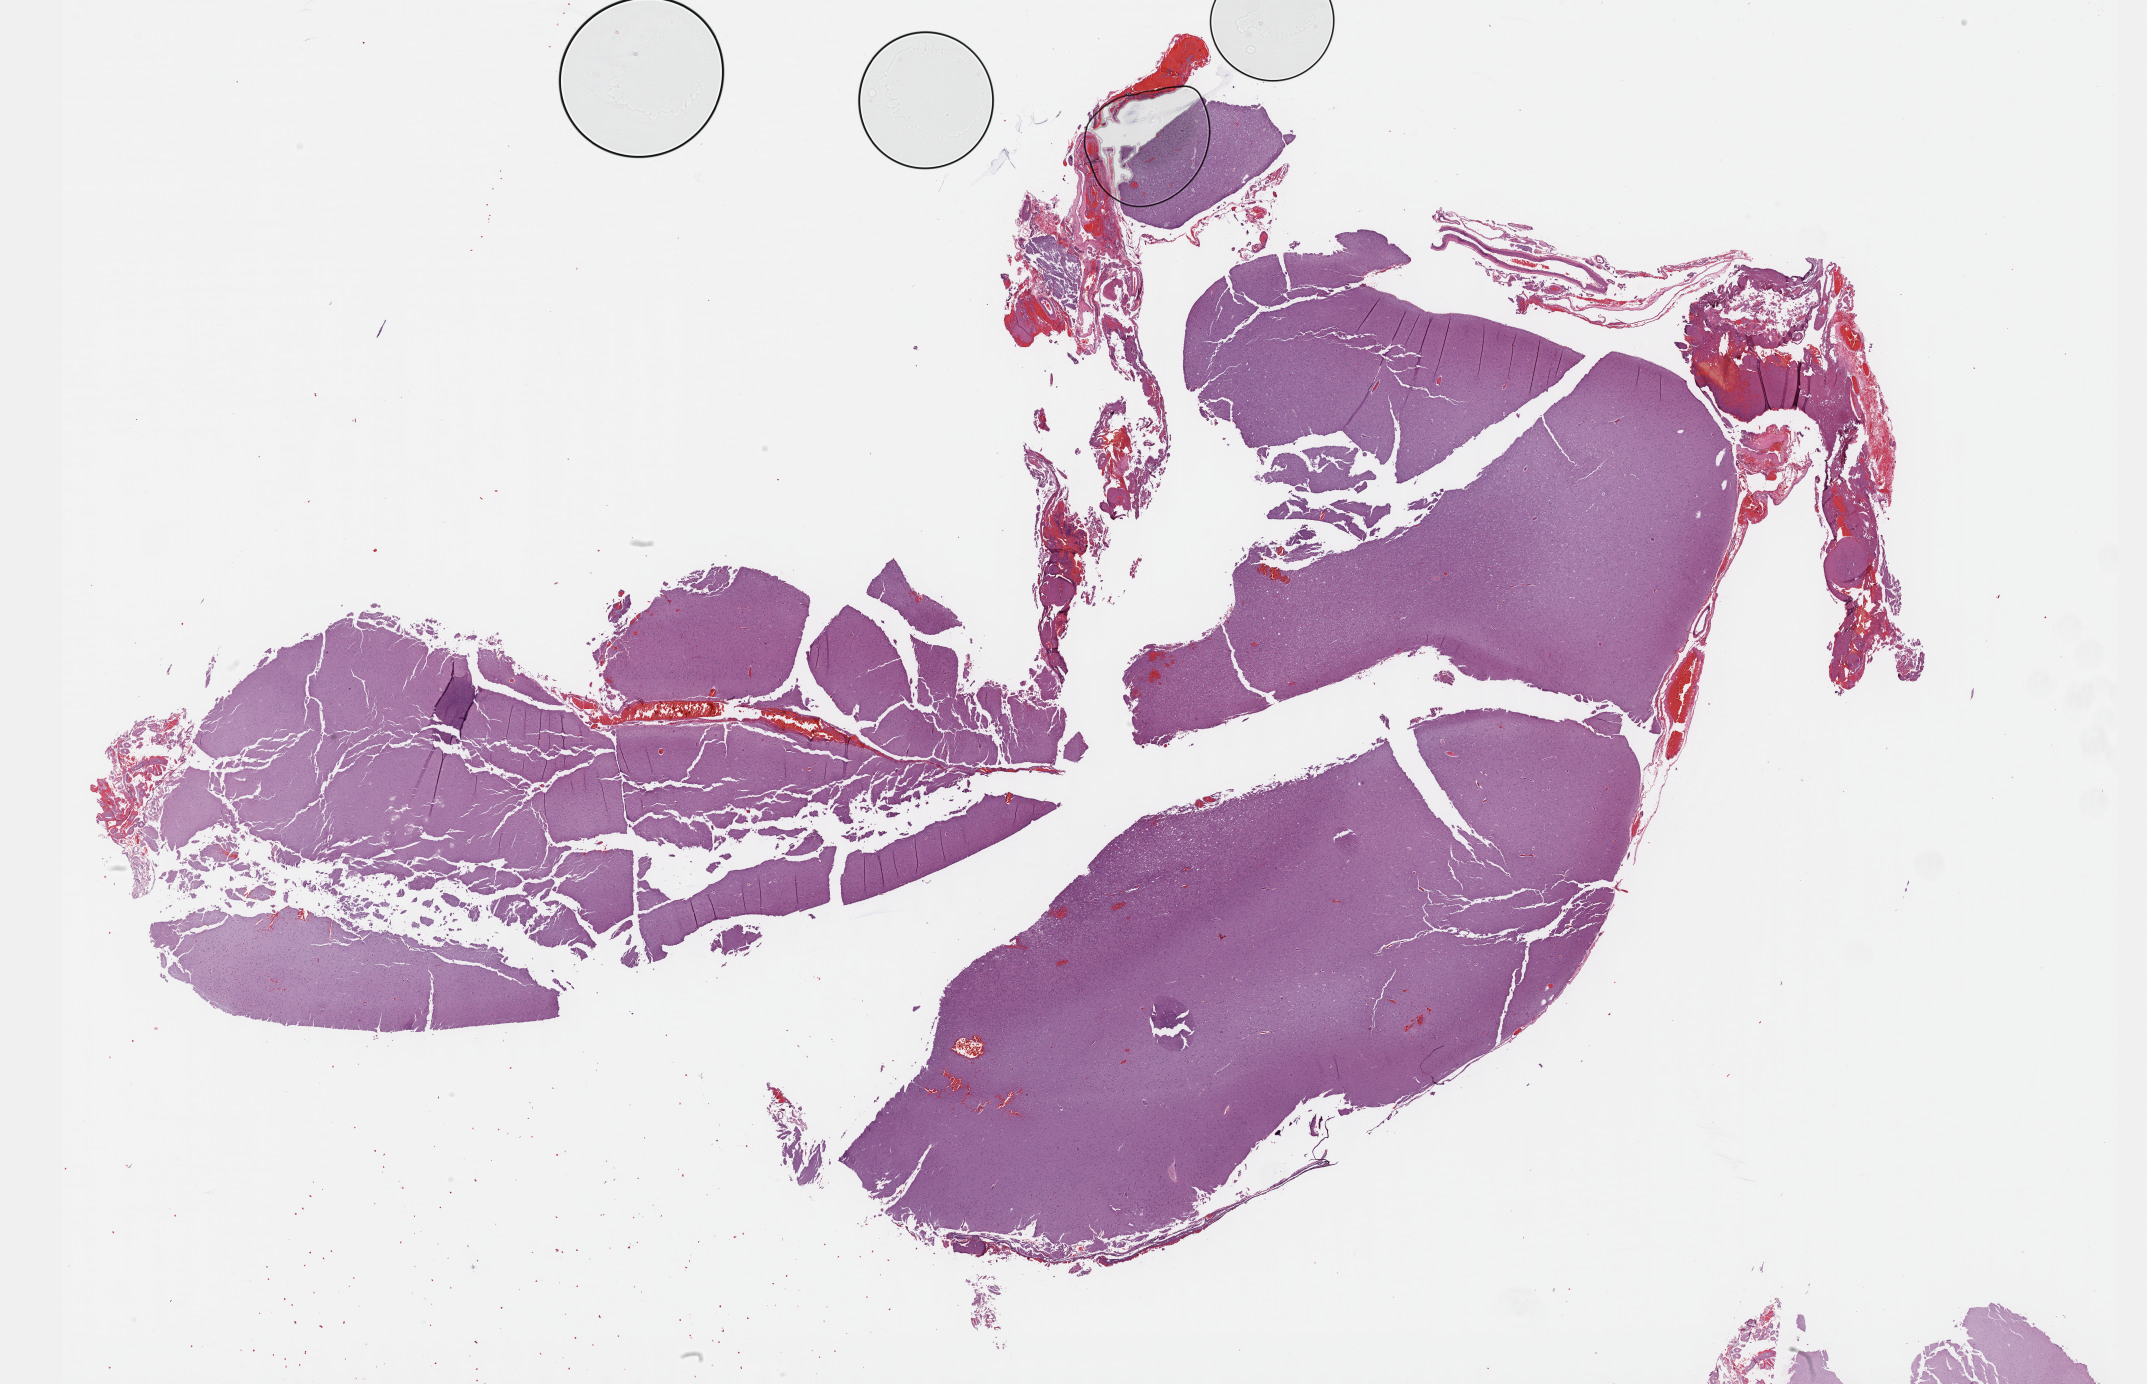
Digitized H&E-stained tissue section (whole slide) — low-resolution overview of the scanned area, about 34.7 x 22.4 mm, formalin-fixed paraffin-embedded (FFPE) diagnostic section, primary tumour sample from the brain. Male, age 35 years at initial diagnosis. Histologic grade: G3 (poorly differentiated).
Pathologic diagnosis: Oligodendroglioma, anaplastic (cerebrum).